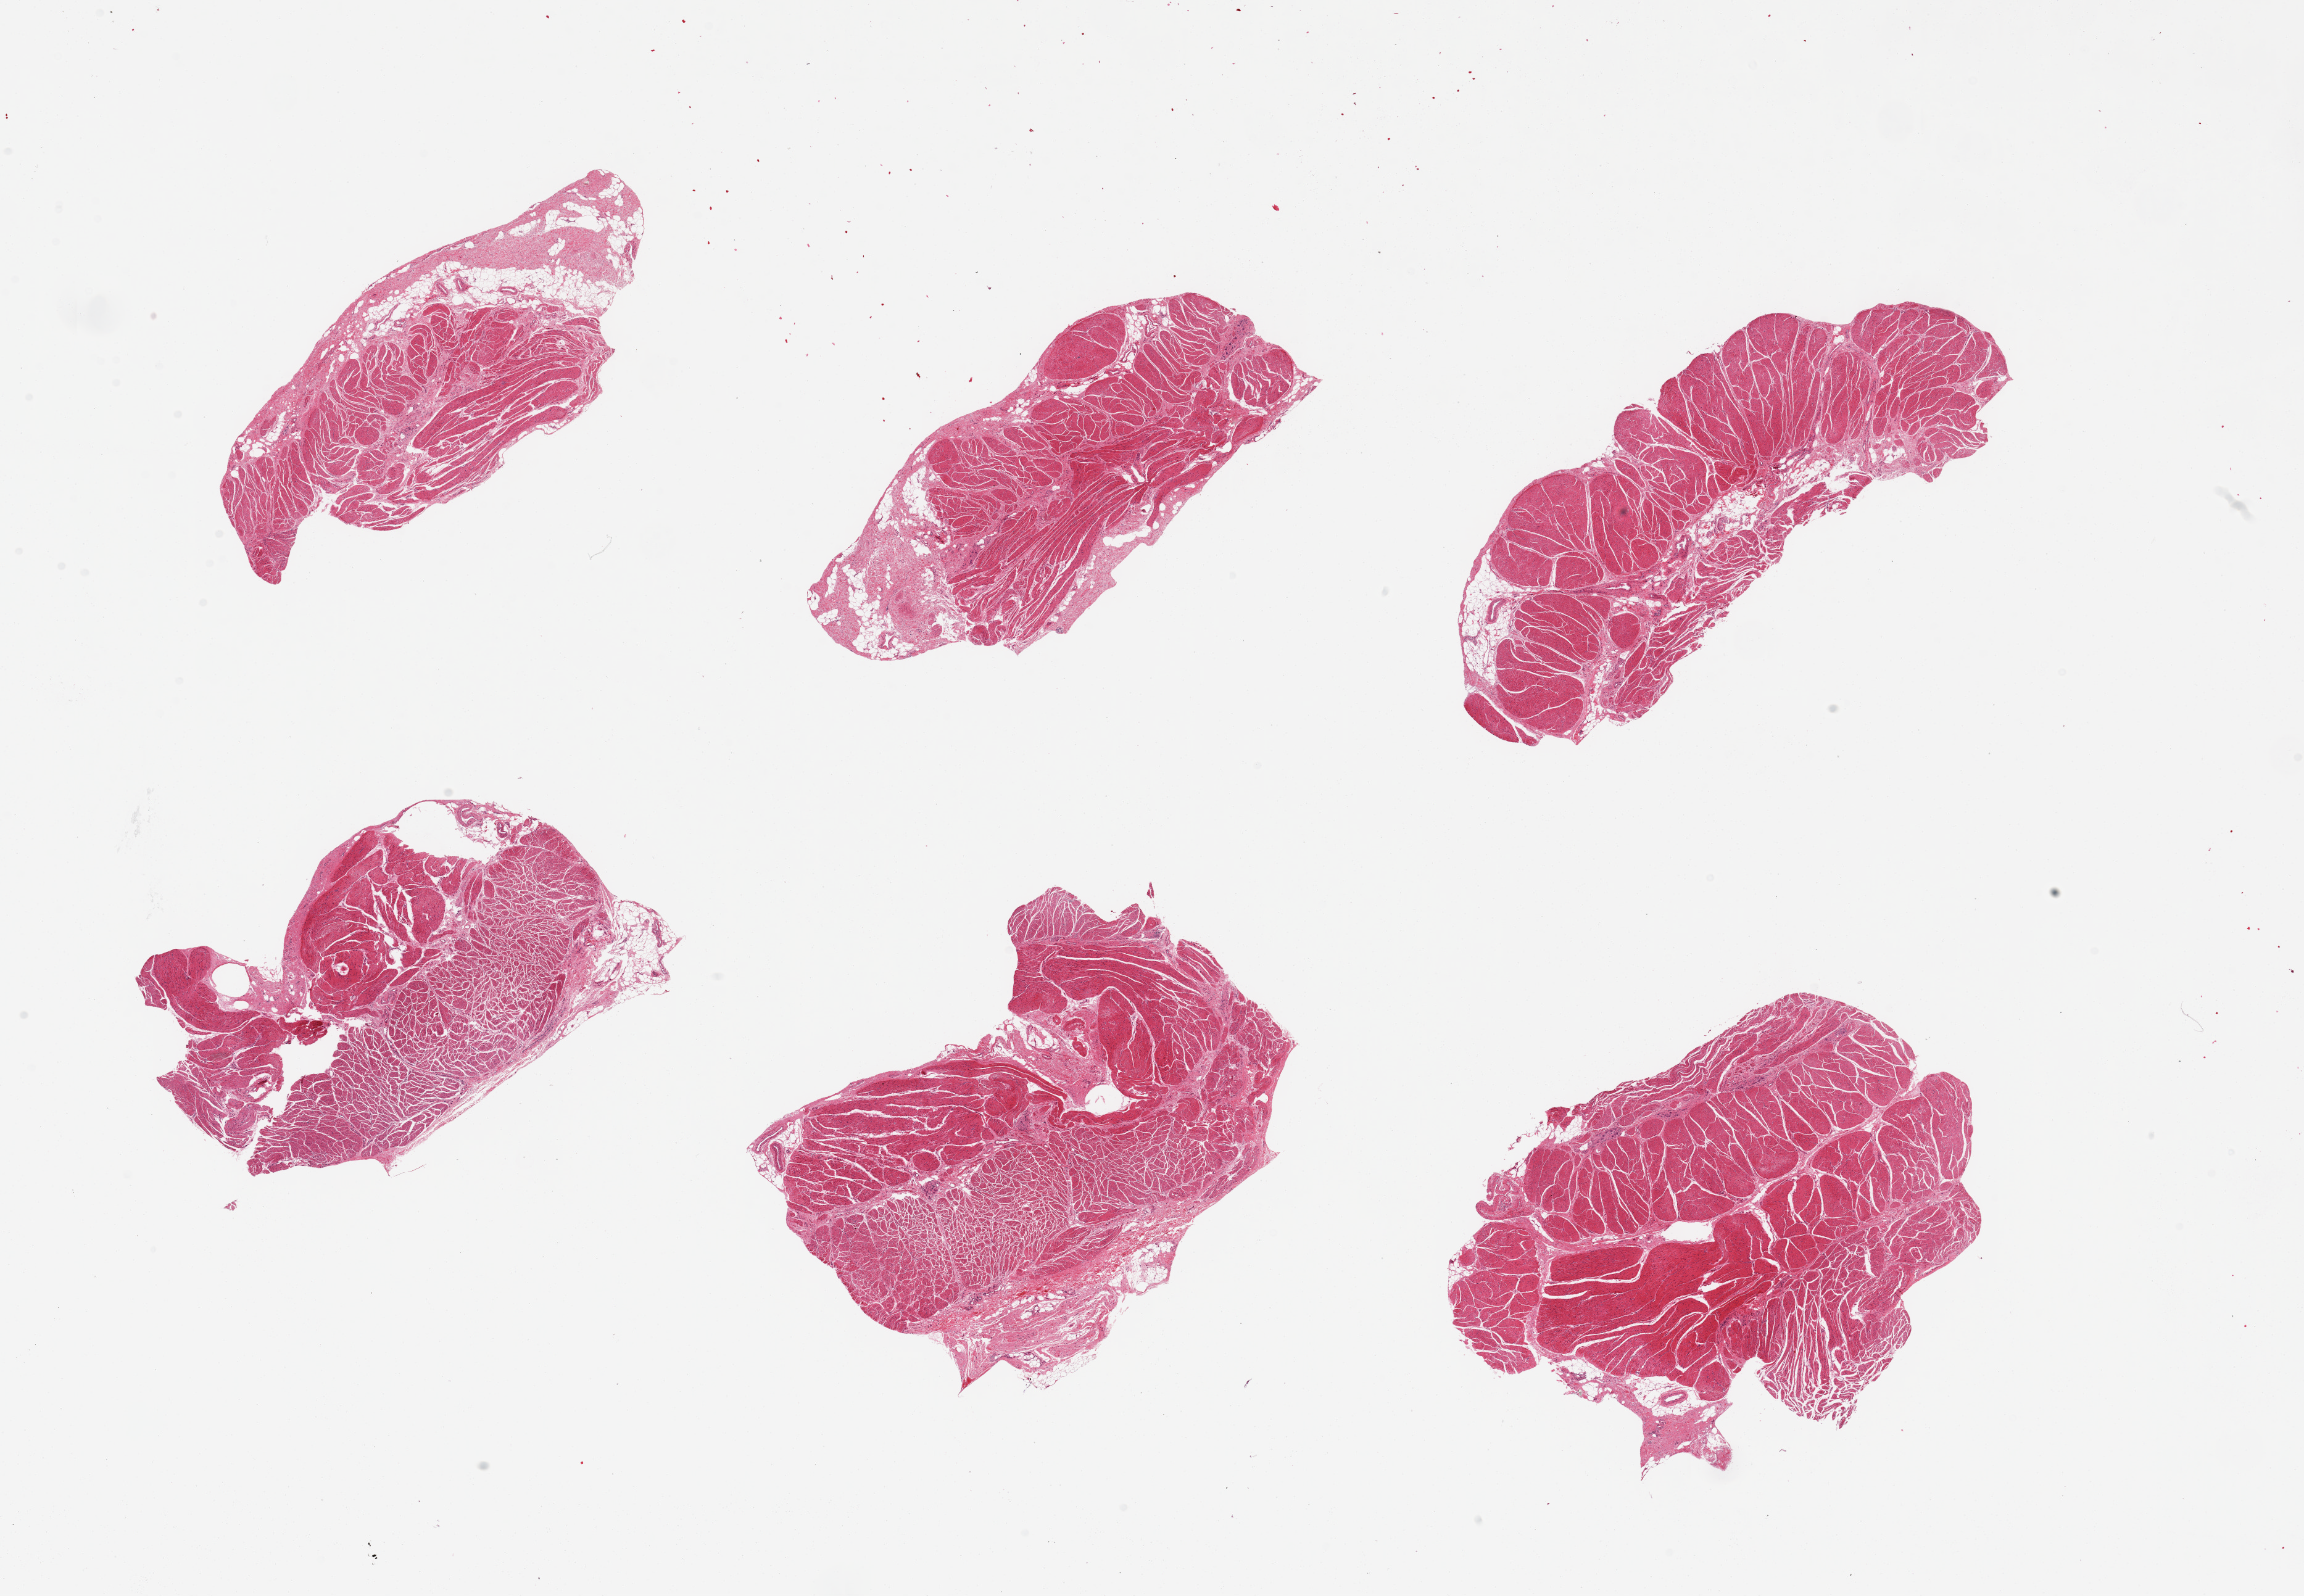
Whole-slide image, H&E stain, a low-resolution overview of the entire scanned area, about 29.5 x 20.5 mm; PAXgene-fixed, paraffin-embedded tissue; sampled site (target tissue): gastroesophageal junction; tissue donor sample. Donor: male.
Pathologist's review note for this sample: 6 pieces; 10% extraneous fibrofatty tissue.